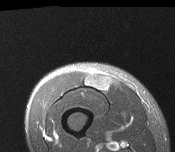
MRI of an extremity soft-tissue mass, one axial slice. Slice 37 of 116 in the series (ordered by position). T2-weighted fat-saturated. MR volume resampled by the dataset authors to the PET/CT grid (not the native acquisition matrix). 3.27 mm slice thickness. 175 × 152 image matrix, field of view 171 × 148 mm. Male patient. Case-level facts recorded for this patient, not image findings: histological type: pleiomorphic leiomyosarcoma; grade: intermediate; site of the primary tumour: right thigh.
Annotated regions visible in this slice (expert contour drawn on MRI and transferred to this co-registered scan by the dataset authors):
- gross tumour volume including surrounding oedema: bounding box (x1, y1, x2, y2) in pixels: (85, 76, 109, 91)